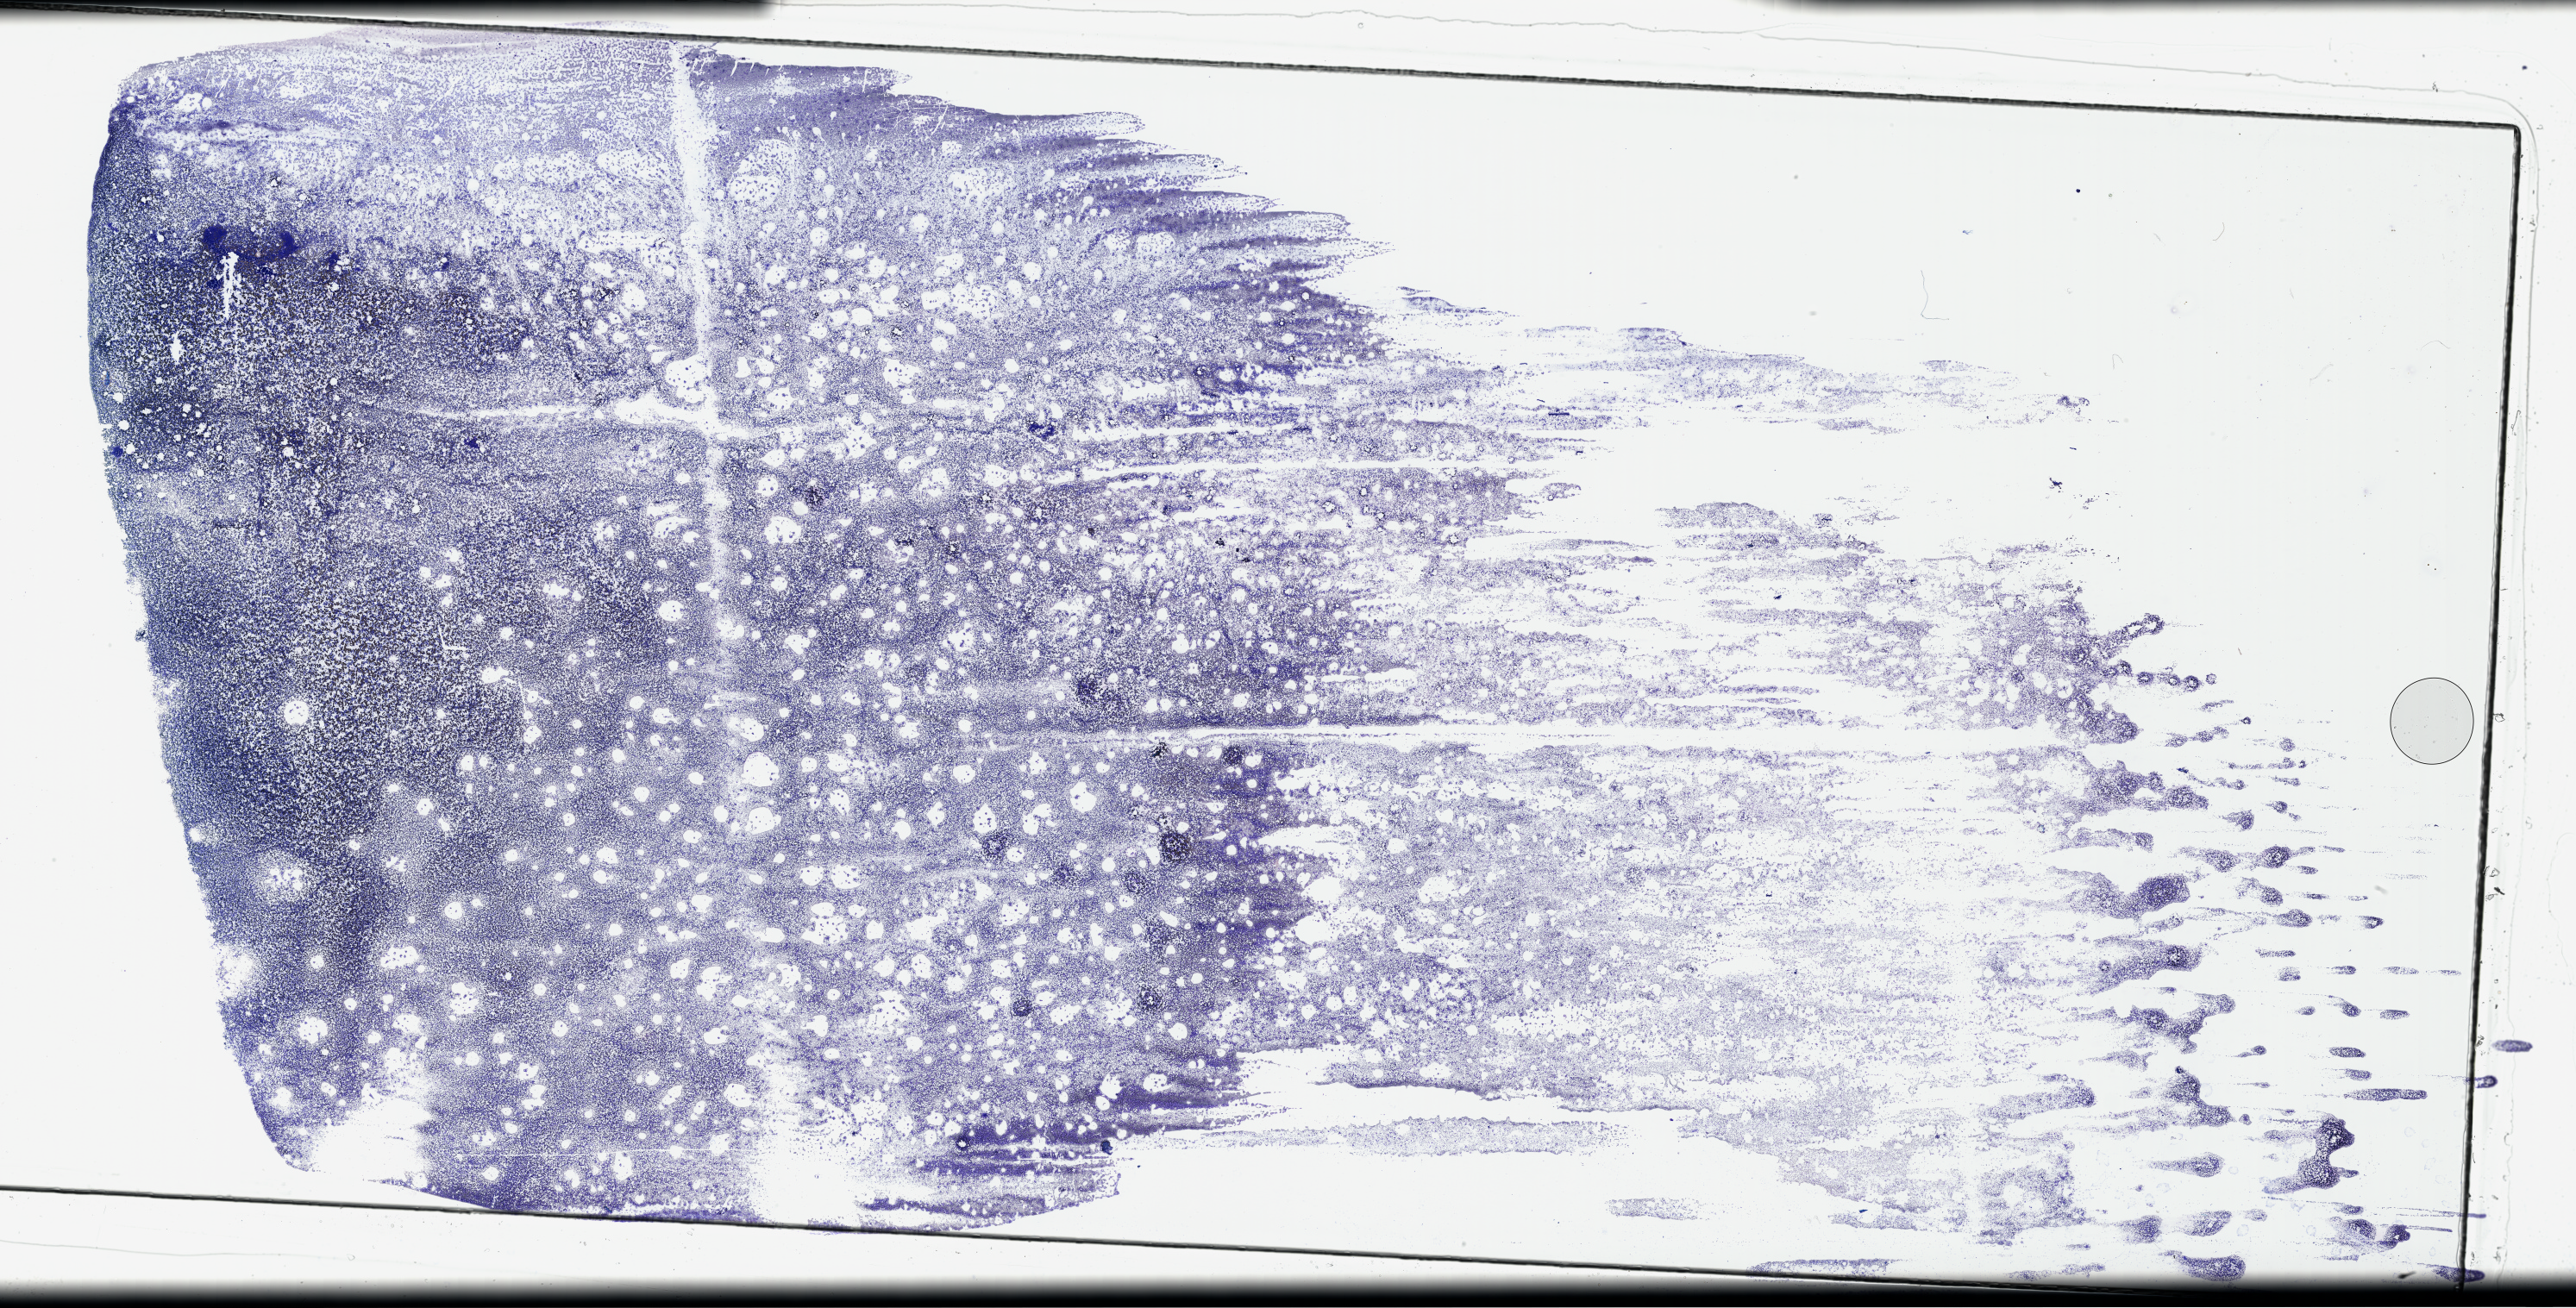
Digitized H&E-stained tissue section (whole slide) — low-resolution overview of the scanned area, about 48.2 x 24.5 mm; bone marrow (leukaemic) sample. Female, 29 y/o. Blasts: 80%.
WHO classification: Acute myelomonocytic leukemia. Diagnosis: Acute Myeloid Leukemia. FAB classification: M4.